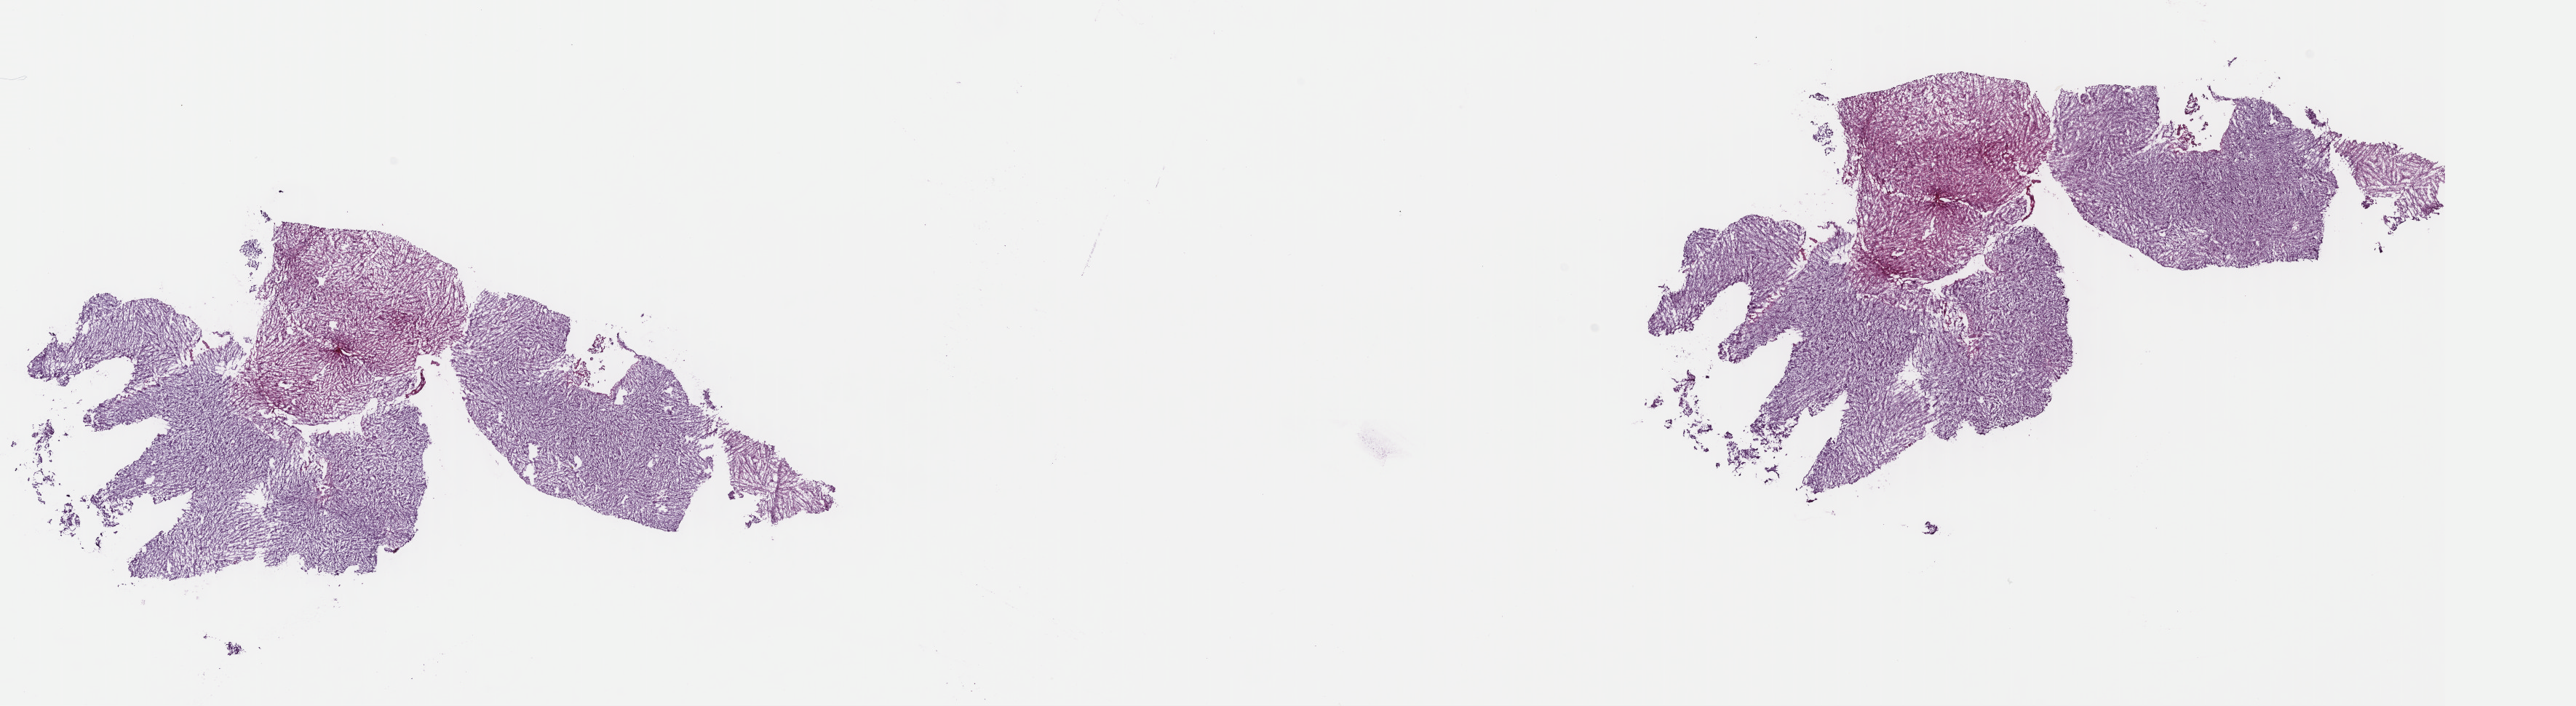
Whole-slide histology image, Hematoxylin and eosin (H&E) stained — low-resolution overview of the scanned area, about 27.8 x 7.6 mm. Frozen section. Primary tumour sample from the brain. Patient: male, age at initial diagnosis 62 years. Histologic grade: G3 (poorly differentiated). Composition of this section per pathologist review: tumour cells 20%, tumour nuclei 70%, normal cells 10%, stromal cells 70%, necrosis 0%. Inflammatory infiltration, as recorded: lymphocyte infiltration 0%, monocyte infiltration 0%, neutrophil infiltration 0%.
Pathologic diagnosis: Astrocytoma, anaplastic (cerebrum).